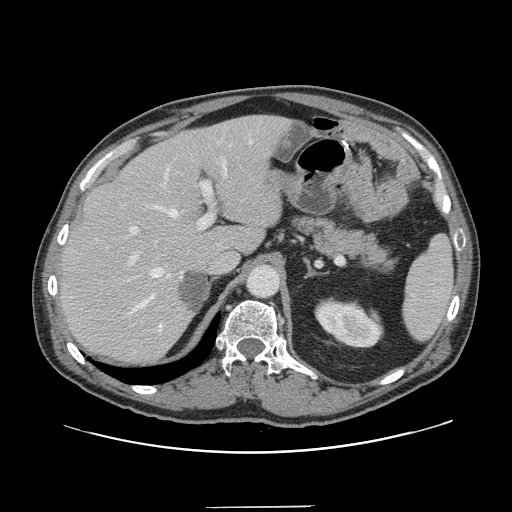
Contrast-enhanced abdominal CT, one axial slice. Slice 100 of 139 in the series (ordered by position). 120 kVp. Intravenous contrast given. Soft-tissue window (W 400 / L 40 HU). 2.5 mm slice thickness. 512 × 512 image matrix. Male patient, age 64 years. Case-level facts recorded for this patient, not image findings: diagnosis: colorectal cancer liver metastases, imaged before liver resection.
Structures marked on this image (outlined manually by an expert reader):
- hepatic veins: box from (x=133, y=140) to (x=253, y=332) px
- liver: (x=61, y=116)–(x=287, y=363)
- planned liver remnant (the part of the liver to remain after resection): (x=60, y=116)–(x=275, y=363)
- portal vein (with intrahepatic branches): (x=129, y=145)–(x=231, y=273)
- liver metastasis: (x=180, y=272)–(x=208, y=312)